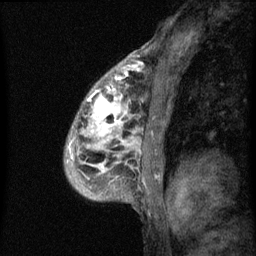
Breast MRI (dynamic contrast-enhanced), one sagittal slice; slice 40 of 60 in the series (ordered by position); dynamic contrast-enhanced series, image 2 of 3 at this slice position (ordered by acquisition); 1.5 T; TE 4.2 ms, TR 8 ms; 256 × 256 image matrix. Patient: female, 50 years.
Structures marked on this image (semi-automatic segmentation, software-assisted and operator-edited):
- analysis volume of interest (the breast-tissue region the enhancement analysis was run in; not a lesion): box from (x=66, y=64) to (x=141, y=187) px
- tumour enhancement mask (voxels above the 70 % enhancement threshold inside the analysis volume of interest): (x=87, y=64)–(x=141, y=173)